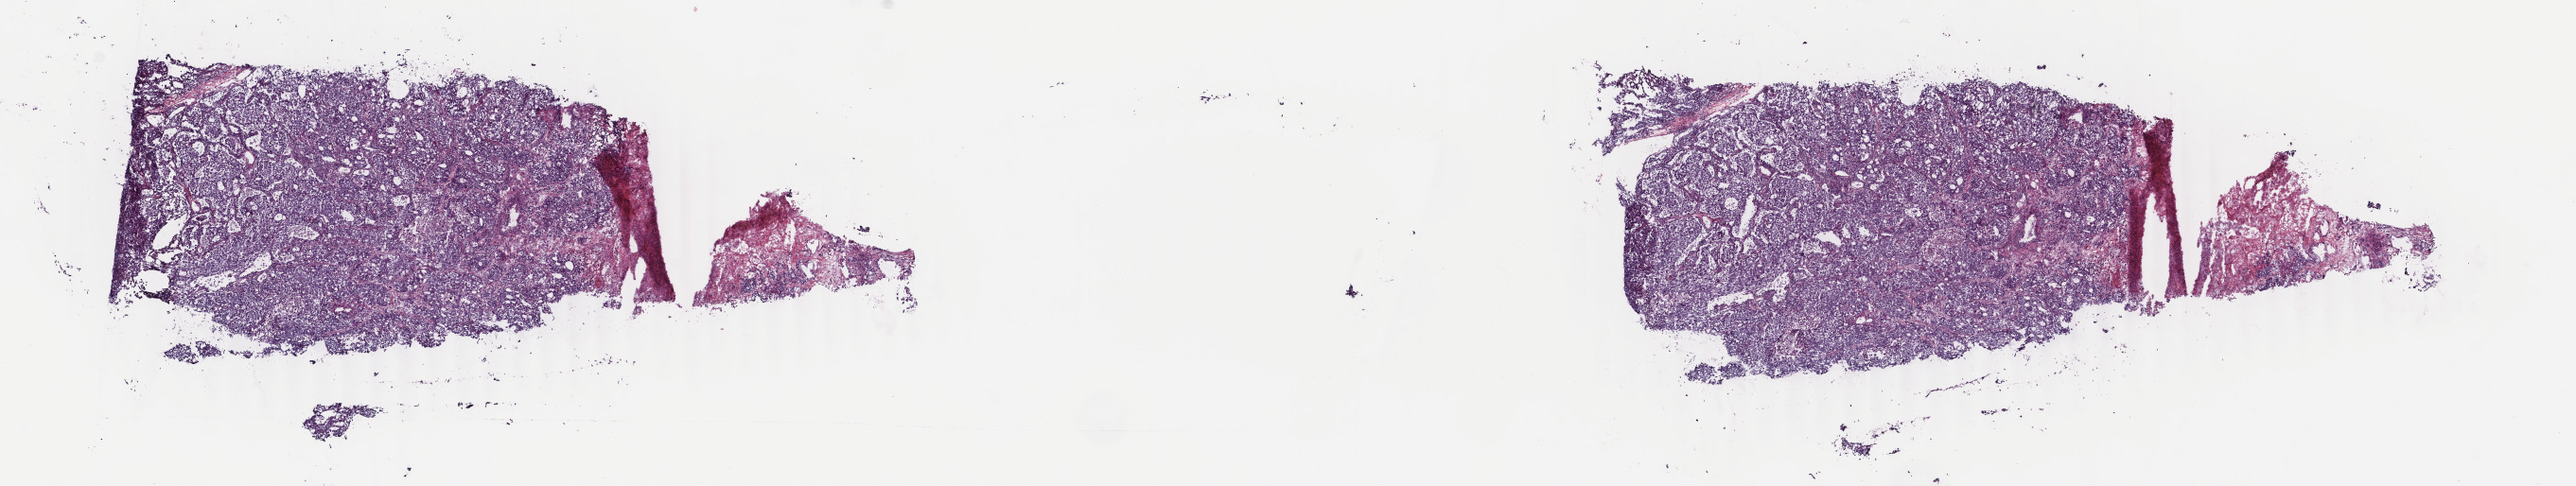
H&E whole-slide image — whole scanned area (about 21.7 x 4.1 mm) shown as a low-resolution overview; frozen section; sample: primary tumour, lung. Female, age 58 years at initial diagnosis. Pathologist review of this section (percent, as recorded): tumour cells 85%, tumour nuclei 88%, normal cells 0%, stromal cells 0%, necrosis 15%. Inflammatory infiltration, as recorded: lymphocyte infiltration 0%, monocyte infiltration 0%, neutrophil infiltration 0%.
- laterality: right
- TNM: T2b N0 M0
- histologic diagnosis: Adenocarcinoma, NOS
- AJCC pathologic stage: IIA